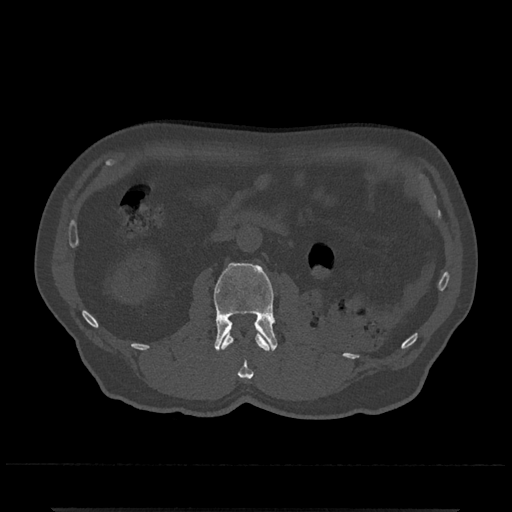
CT including the spine, one axial slice. Slice 311 of 797 in the series (ordered by position). 120 kVp. Bone window (W 1800 / L 400 HU). 512 × 512 image matrix, field of view 393 × 393 mm. Patient: male, 67 years. Case-level facts recorded for this patient, not image findings: primary cancer: prostate.
Structures marked on this image (semi-automatically segmented with operator editing):
- L1 vertebra: box from (x=221, y=332) to (x=270, y=379) px
- L2 vertebra: (x=214, y=262)–(x=278, y=352)